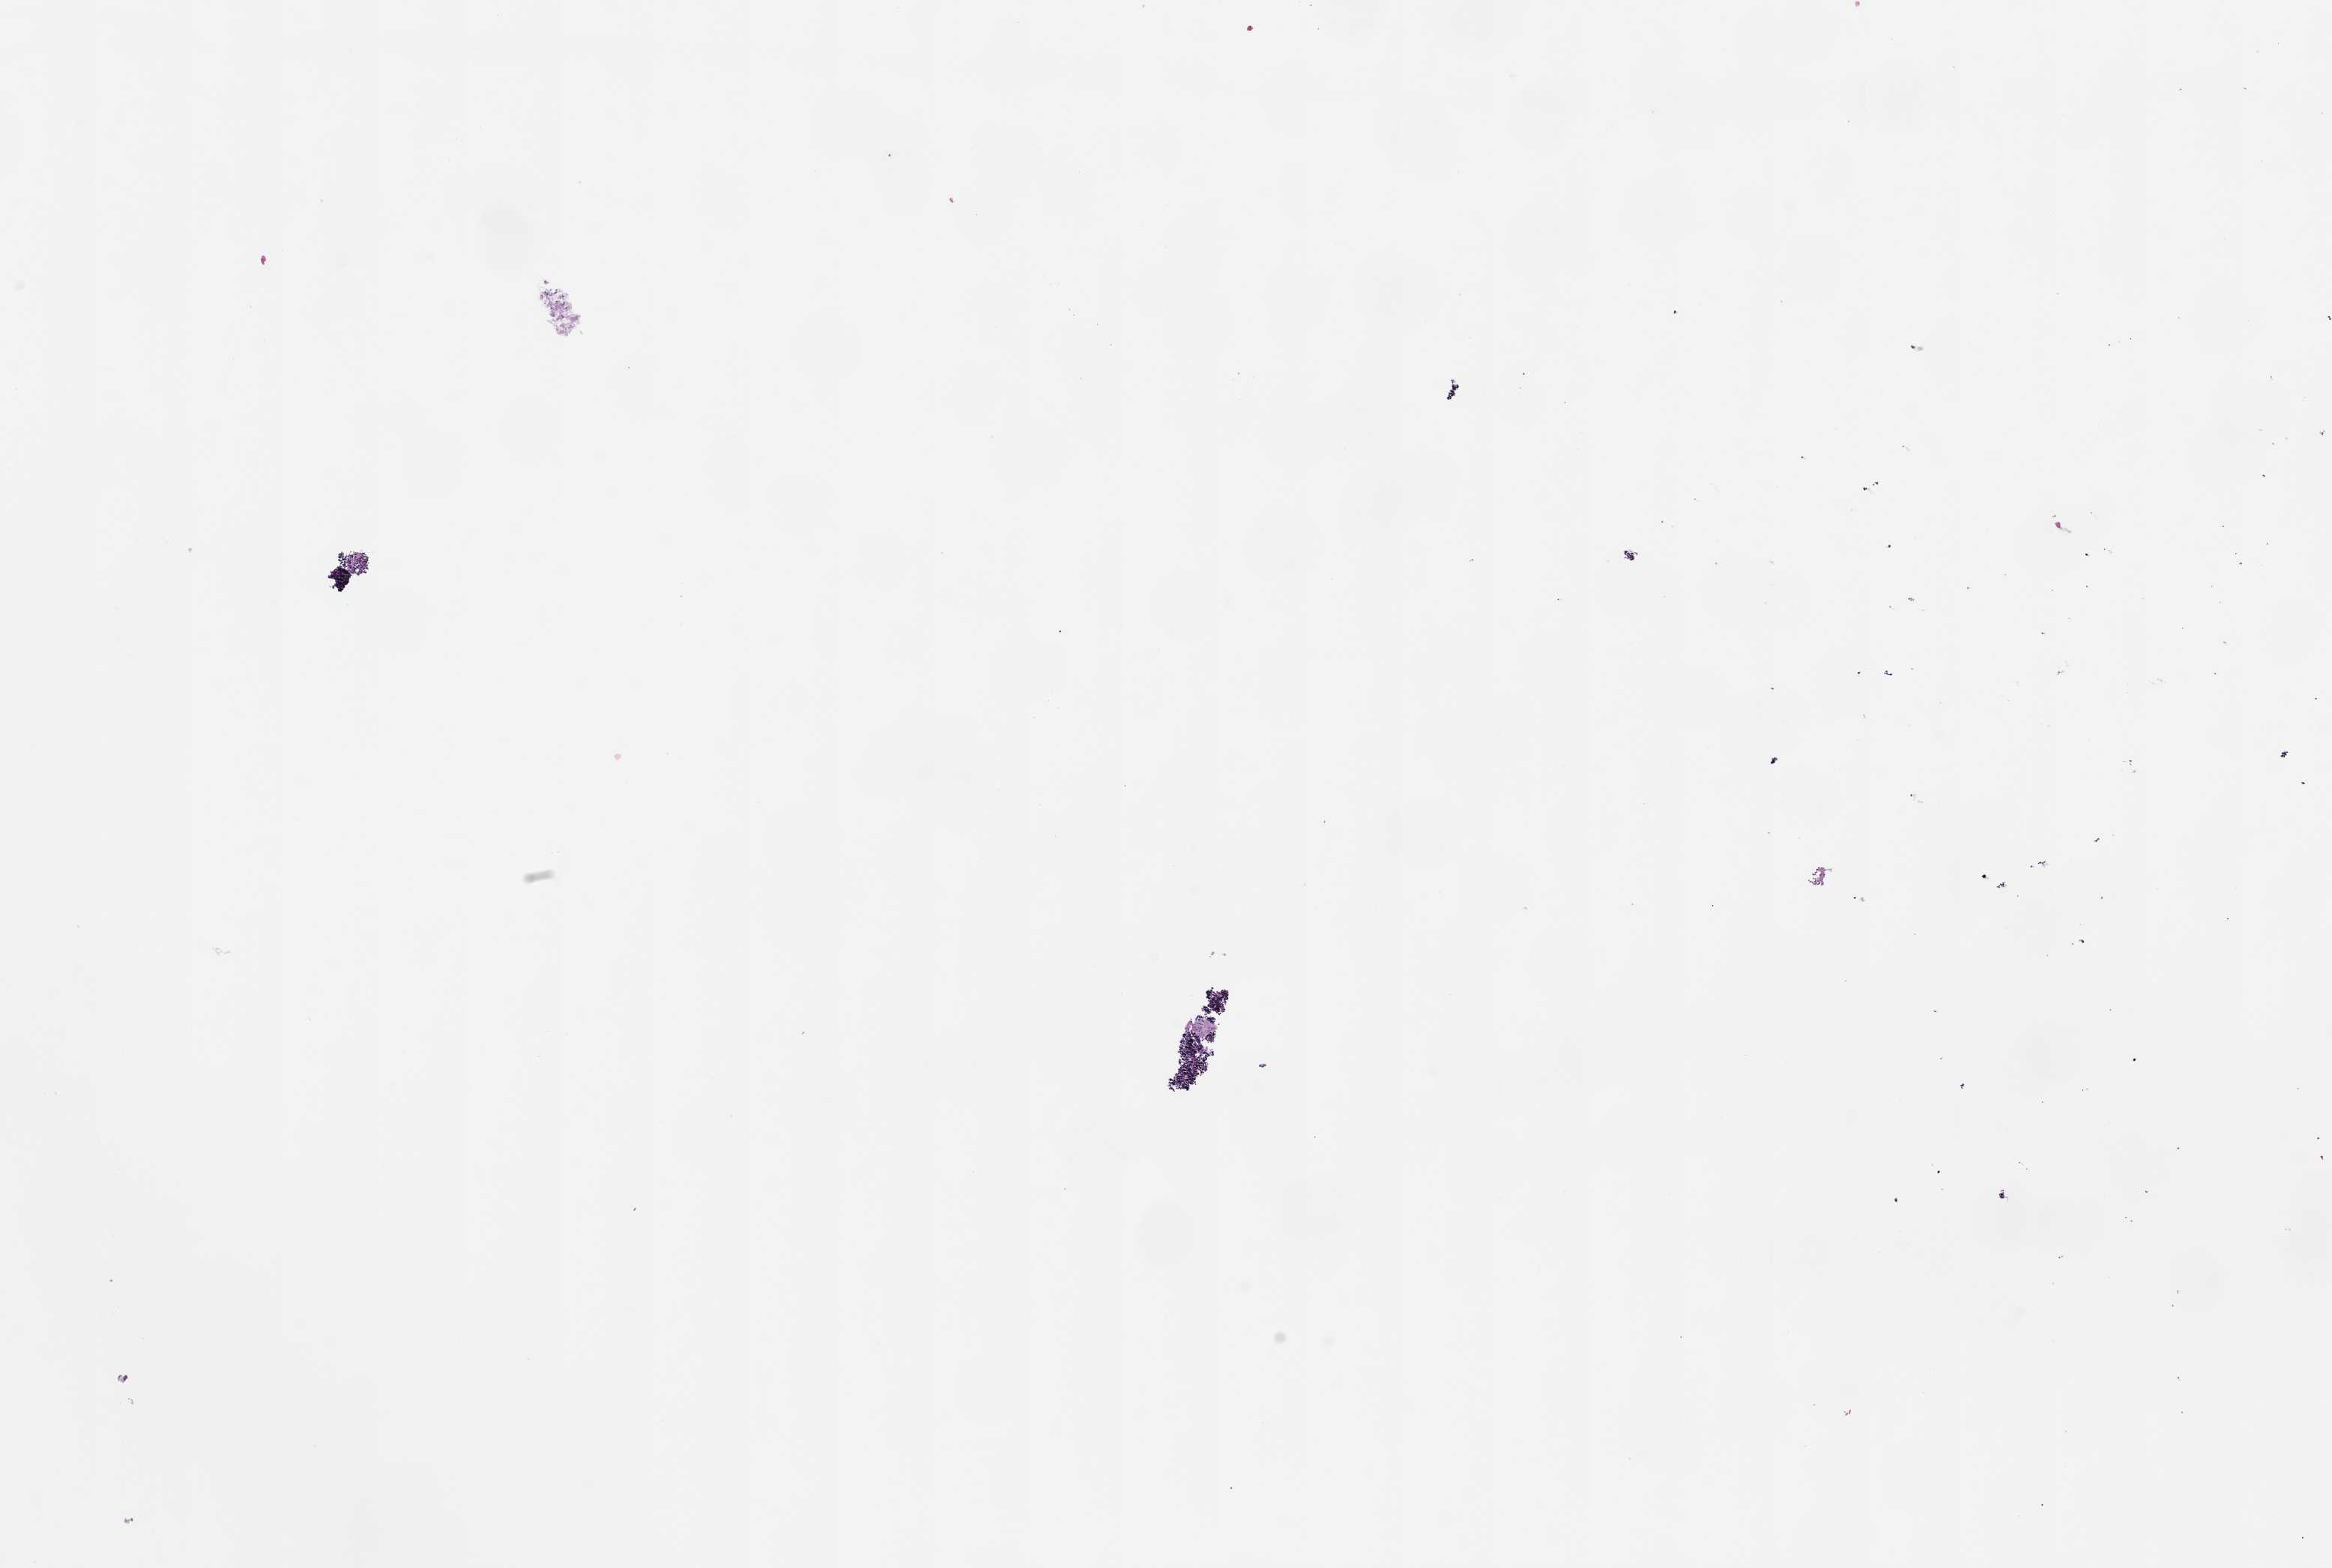
H&E whole-slide image, a low-resolution overview of the entire scanned area, about 12.6 x 8.5 mm. Formalin-fixed, paraffin-embedded (FFPE) tissue. Specimen time point: collected at baseline (before treatment). Patient: female.
* this section: metastatic tumor tissue
* patient diagnosis (primary): Small Cell Lung Carcinoma